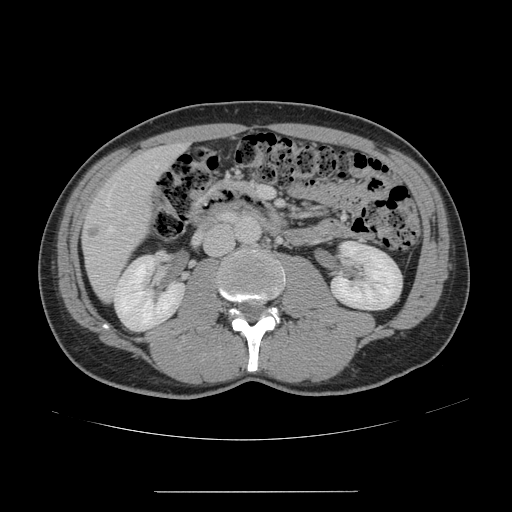
Contrast-enhanced abdominal CT, one axial slice. Position 51 of 178 along the scan axis. Intravenous contrast given. Soft-tissue window (W 400 / L 40 HU). 2.5 mm slice thickness. 512 × 512 image matrix, field of view 401 × 401 mm. Male patient, age 53 years. From the clinical record (not read from this slice): diagnosis: colorectal cancer liver metastases, imaged before liver resection; multiple liver metastases: yes; largest metastasis: 2.4 cm; chemotherapy before resection: yes.
Structures marked on this image (outlined manually by an expert reader):
- hepatic veins: bounding box (x1, y1, x2, y2) in pixels: (101, 166, 158, 236)
- liver: (83, 147, 179, 298)
- portal vein (with intrahepatic branches): (258, 186, 267, 198)
- liver metastasis: (85, 228, 98, 240)